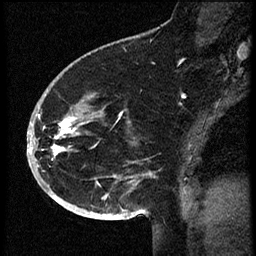
Breast MRI (dynamic contrast-enhanced), one sagittal slice. Slice 39 of 60 in the series (ordered by position). Dynamic contrast-enhanced study with each time point stored as its own series, time point 2 of 3 at this slice position (early post-contrast, ordered by acquisition time). 1.5 T. TE 4.2 ms, TR 18.9 ms. 2 mm slice thickness. 256 × 256 image matrix. Female patient. Case-level facts recorded for this patient, not image findings: setting: breast cancer imaged before/during neoadjuvant chemotherapy; receptor status: HR-positive, HER2-negative.
Outlined on this slice (semi-automatic segmentation, software-assisted and operator-edited):
- analysis volume of interest (the breast-tissue region the enhancement analysis was run in; not a lesion): box from (x=30, y=87) to (x=106, y=173) px
- tumour enhancement mask (voxels above the 100 % enhancement threshold inside the analysis volume of interest): (x=30, y=118)–(x=84, y=153)